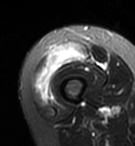
MRI of an extremity soft-tissue mass, one axial slice; position 13 of 95 along the scan axis; T2-weighted fat-saturated; MR volume resampled by the dataset authors to the PET/CT grid (not the native acquisition matrix); 3.27 mm slice thickness; 135 × 146 image matrix. Female patient. From the clinical record (not read from this slice): histological type: pleiomorphic undifferentiated sarcoma; grade: high; site of the primary tumour: right quadricep.
Structures marked on this image (expert contour drawn on MRI and transferred to this co-registered scan by the dataset authors):
- gross tumour volume including surrounding oedema: bounding box <34,45,88,99> (left, top, right, bottom; pixels)